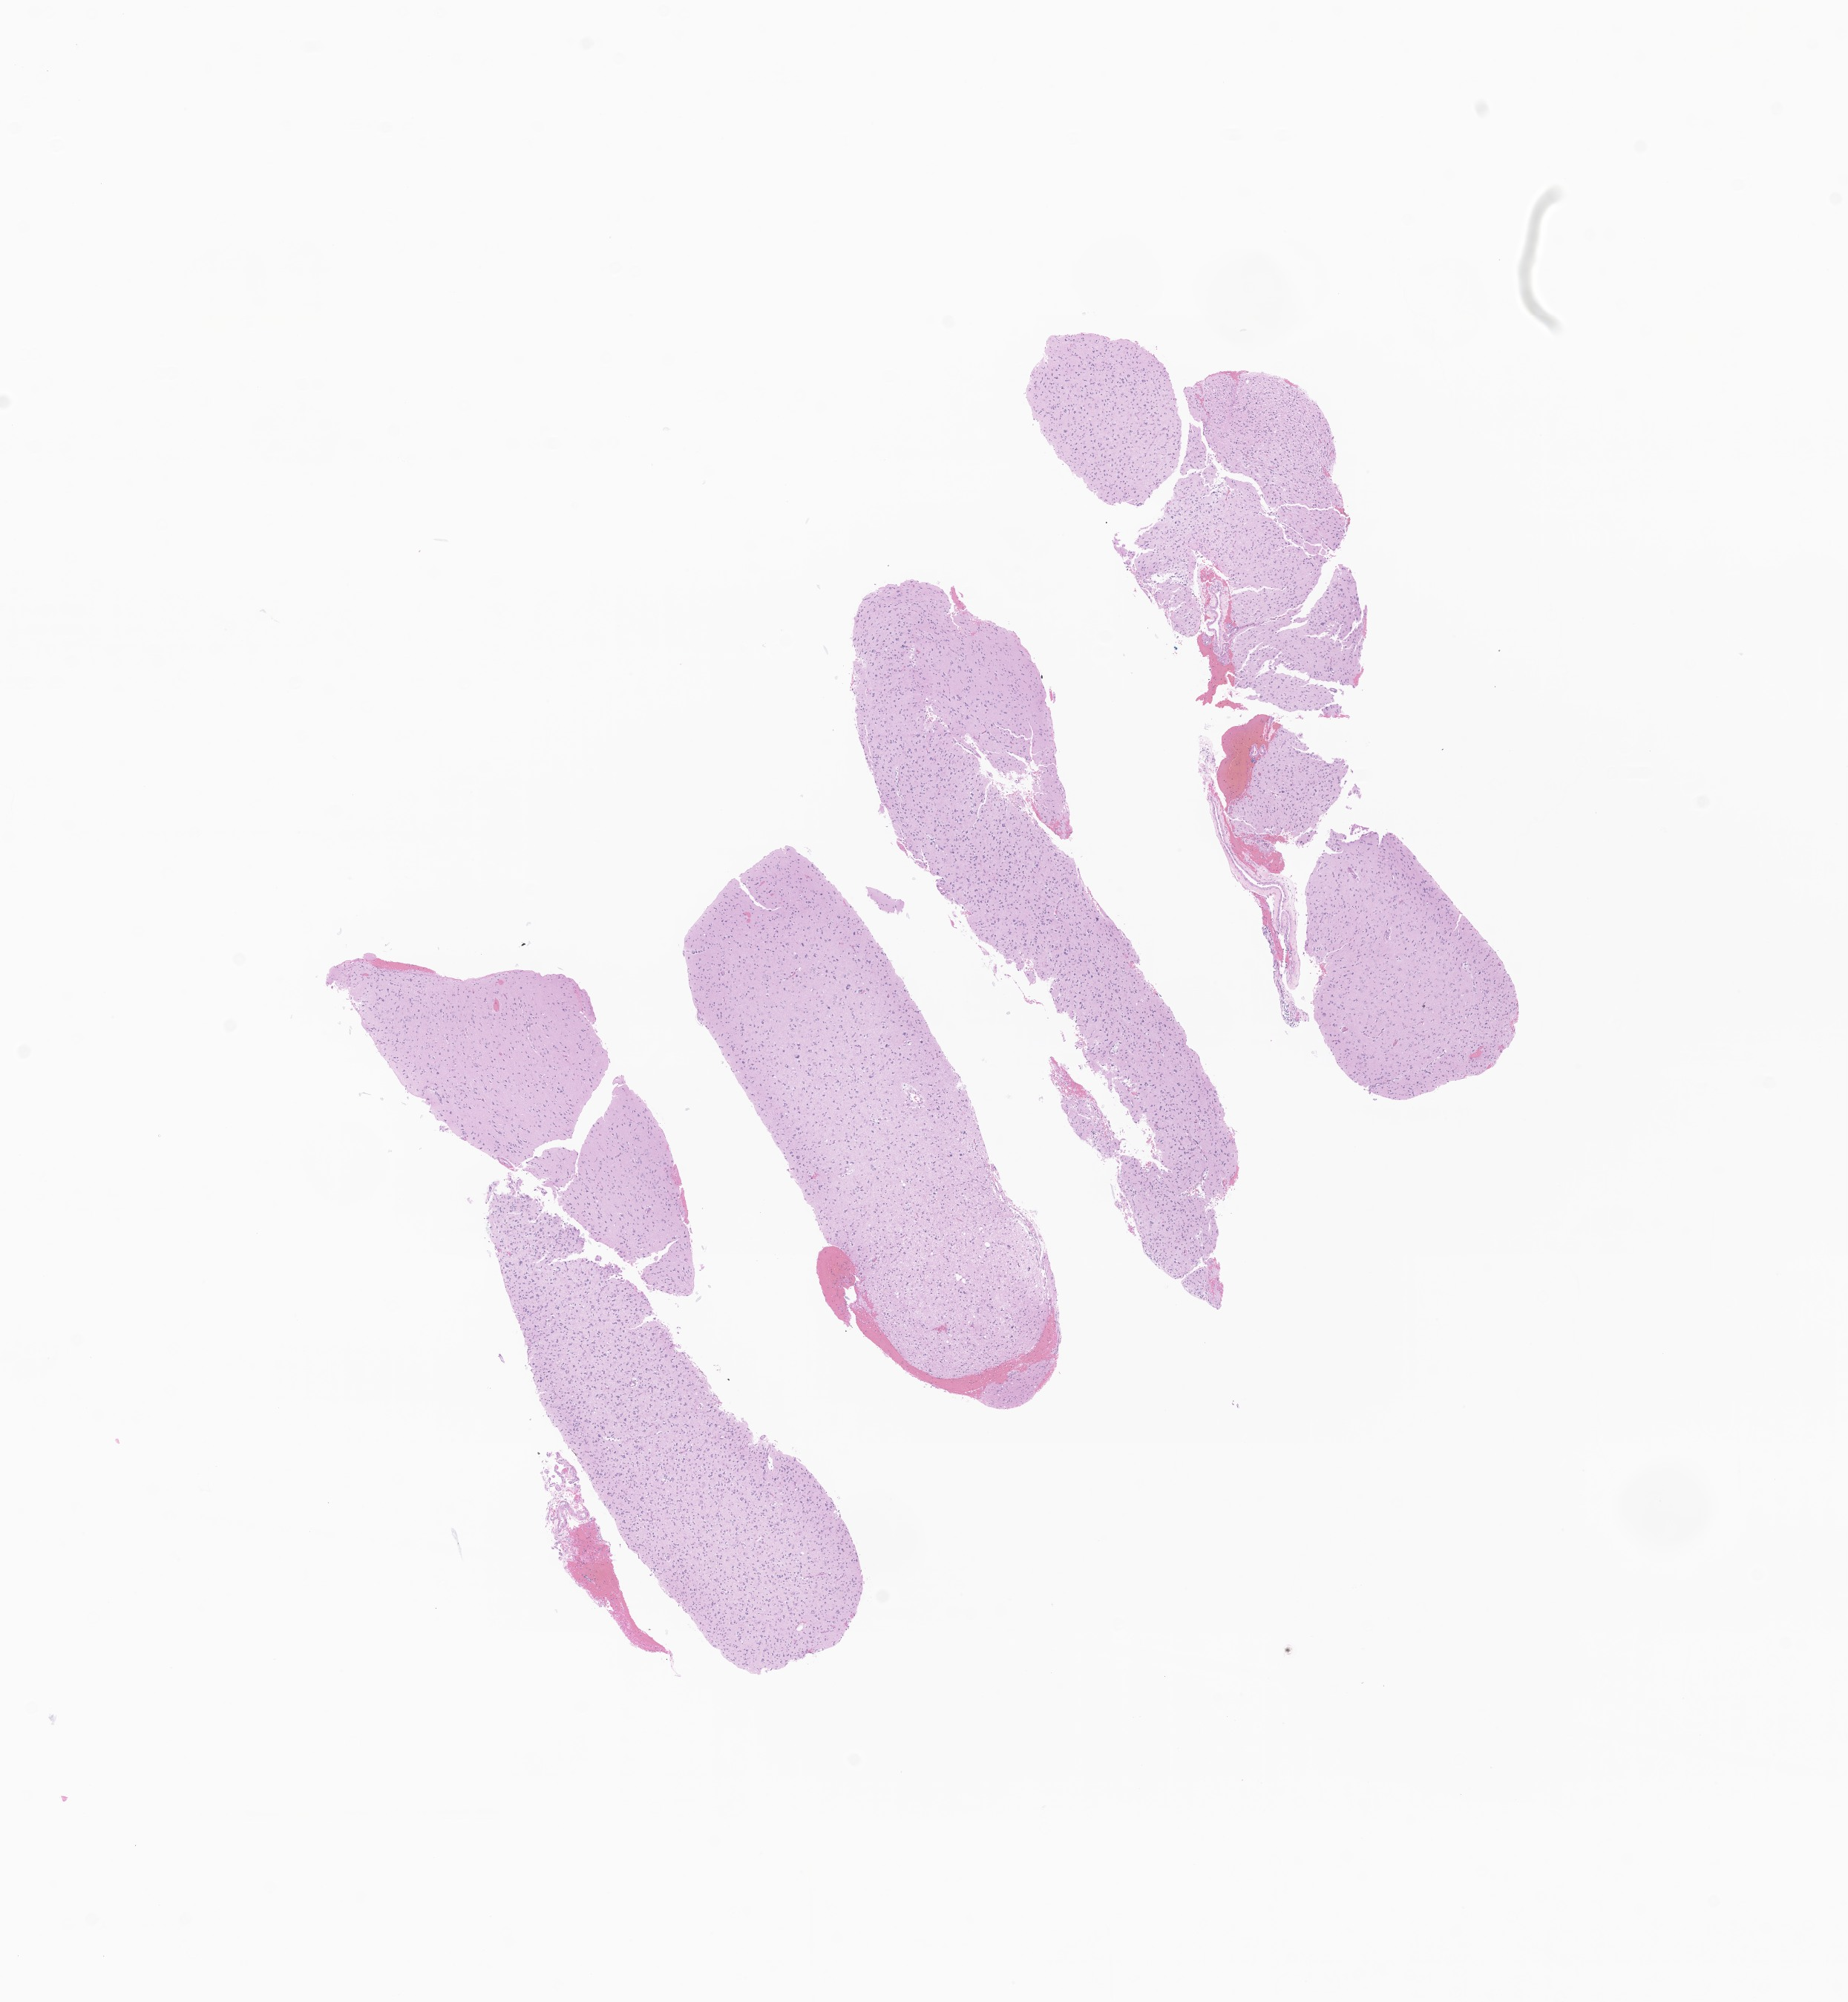
Whole-slide image, haematoxylin and eosin stain of tumor tissue from the parietal lobe — a low-resolution overview of the entire scanned area, about 10.5 x 11.4 mm, formalin-fixed, paraffin-embedded (FFPE) tissue. Patient: female, age 310 months (25 years 10 months).
* diagnosis (ICD-O-3 morphology term): Glioma, malignant